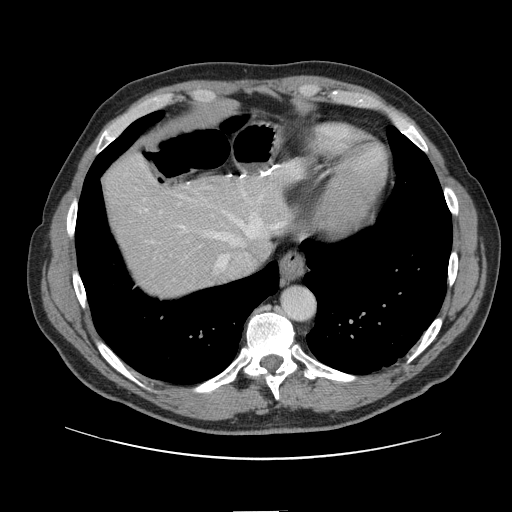
Contrast-enhanced abdominal CT, one axial slice; slice 125 of 161 in the series (ordered by position); intravenous contrast given; soft-tissue window (W 400 / L 40 HU); 2.5 mm slice thickness; 512 × 512 image matrix, field of view 412 × 412 mm. Male patient, age 66 years. Case-level facts recorded for this patient, not image findings: diagnosis: colorectal cancer liver metastases, imaged before liver resection; multiple liver metastases: no; largest metastasis: 3.5 cm; chemotherapy before resection: yes.
Outlined on this slice (expert manual segmentation):
- hepatic veins: bounding box (x1, y1, x2, y2) in pixels: (141, 183, 286, 273)
- liver: (105, 156, 300, 296)
- planned liver remnant (the part of the liver to remain after resection): (105, 157, 302, 291)